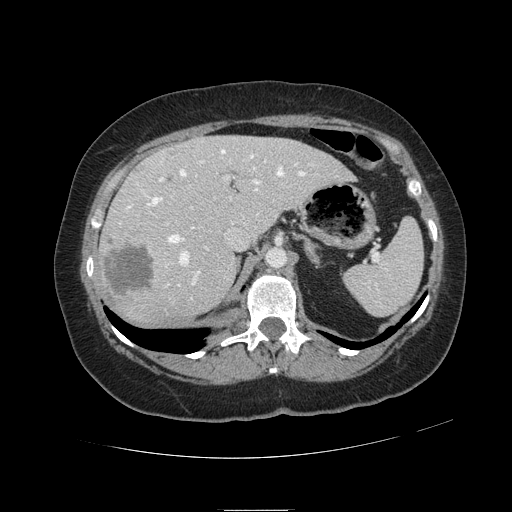
Contrast-enhanced abdominal CT, one axial slice; position 76 of 121 along the scan axis; intravenous contrast given; soft-tissue window (W 400 / L 40 HU); 2.5 mm slice thickness; 512 × 512 image matrix. Female patient, age 52 years. From the clinical record (not read from this slice): diagnosis: colorectal cancer liver metastases, imaged before liver resection; multiple liver metastases: yes; largest metastasis: 6.3 cm; chemotherapy before resection: yes.
Structures marked on this image (expert manual segmentation):
- hepatic veins: box from (x=127, y=150) to (x=305, y=299) px
- liver: (x=100, y=136)–(x=351, y=324)
- planned liver remnant (the part of the liver to remain after resection): (x=167, y=136)–(x=351, y=235)
- portal vein (with intrahepatic branches): (x=120, y=161)–(x=266, y=285)
- liver metastasis: (x=105, y=247)–(x=155, y=296)